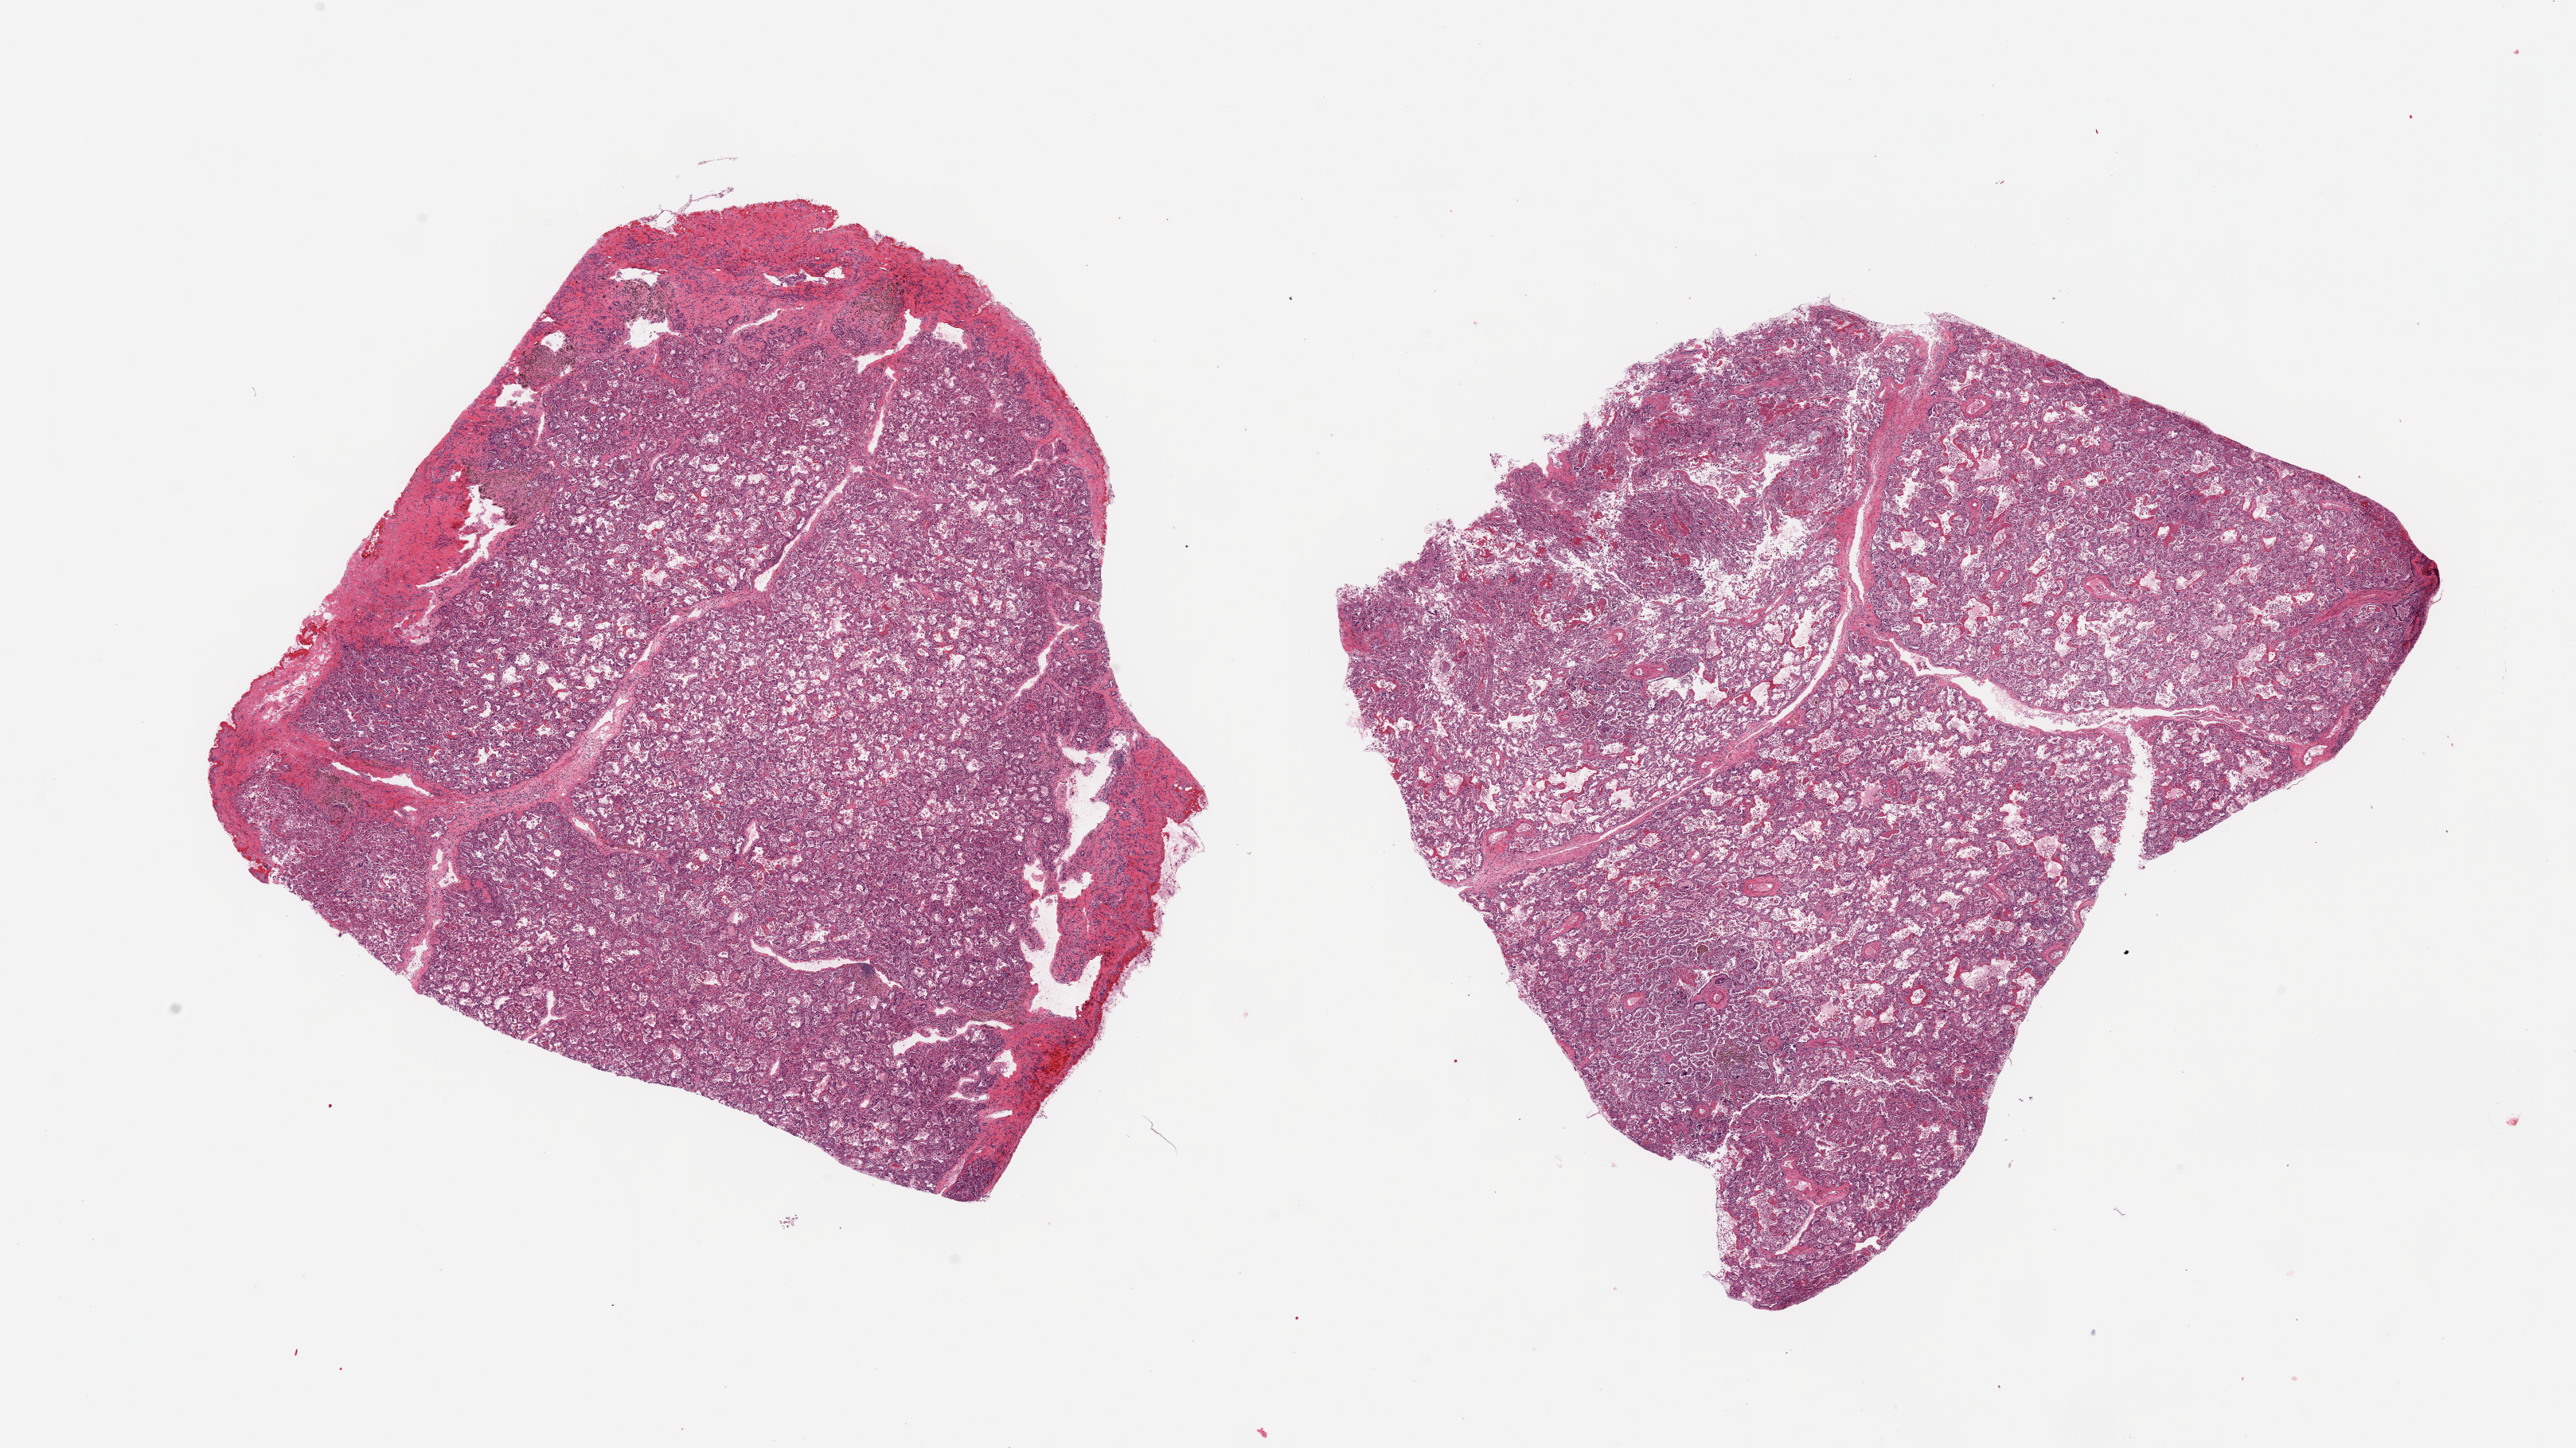
Hematoxylin and eosin (H&E) whole-slide image, shown as a low-resolution overview of the whole scanned area (about 25.6 x 14.4 mm); PAXgene-fixed paraffin-embedded (PFPE) section; section of lung (target tissue); tissue donor sample. Donor: male.
Pathologist's review note for this sample: 2 pieces, diffuse alvoelar damage/ARDS, fibrosing pneumonitis, chronic congestion.